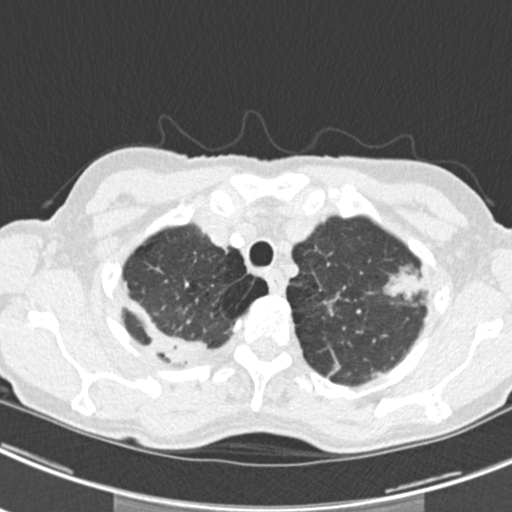
Axial slice from a low-dose chest CT screening exam, second annual screen, lung window (W 1500 / L -600 HU), standard (soft-tissue) reconstruction kernel (B30f), 120 kVp, slice 35 of 219 in the series. Female, age 63 years at enrolment. Current smoker at enrolment.
Lesion marked by an expert reader, box from (x=370, y=254) to (x=433, y=314) px. The screening reader recorded 9 non-calcified nodules or masses ≥4 mm on this exam (left upper lobe, right upper lobe, left upper lobe, left lower lobe, right middle lobe, left lower lobe, left lower lobe, right lower lobe, right lower lobe); which of them this box marks is not recorded. Official screen result: positive, other.